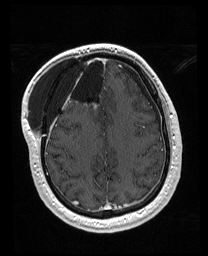
Brain MRI from a brain-tumour surgery series, one axial slice. Position 59 of 176 along the scan axis. T1-weighted post-contrast. 1 mm slice thickness. 208 × 256 image matrix. From the clinical record (not read from this slice): histopathology: Astrocytoma; WHO grade: 4; IDH mutation: yes; tumour location: Right Orbitofrontal Anterior Temporal Insular.
Structures marked on this image (manually delineated by an expert):
- previous resection cavity: bounding box [x1, y1, x2, y2] px = [56, 54, 106, 101]